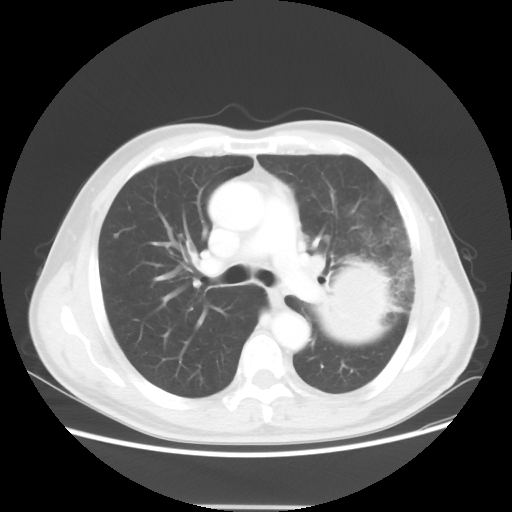
Chest CT, one axial slice; position 33 of 53 along the scan axis; reconstruction kernel STANDARD; lung window (W 1500 / L -600 HU); 5 mm slice thickness; 512 × 512 image matrix. Male patient, age 60 years. Case-level facts recorded for this patient, not image findings: clinical TNM (as recorded): T4 N1 M1a.
Outlined on this slice (bounding box drawn by a radiologist):
- lung tumour (recorded histology: large cell carcinoma): bounding box (x1, y1, x2, y2) in pixels: (303, 253, 401, 352)